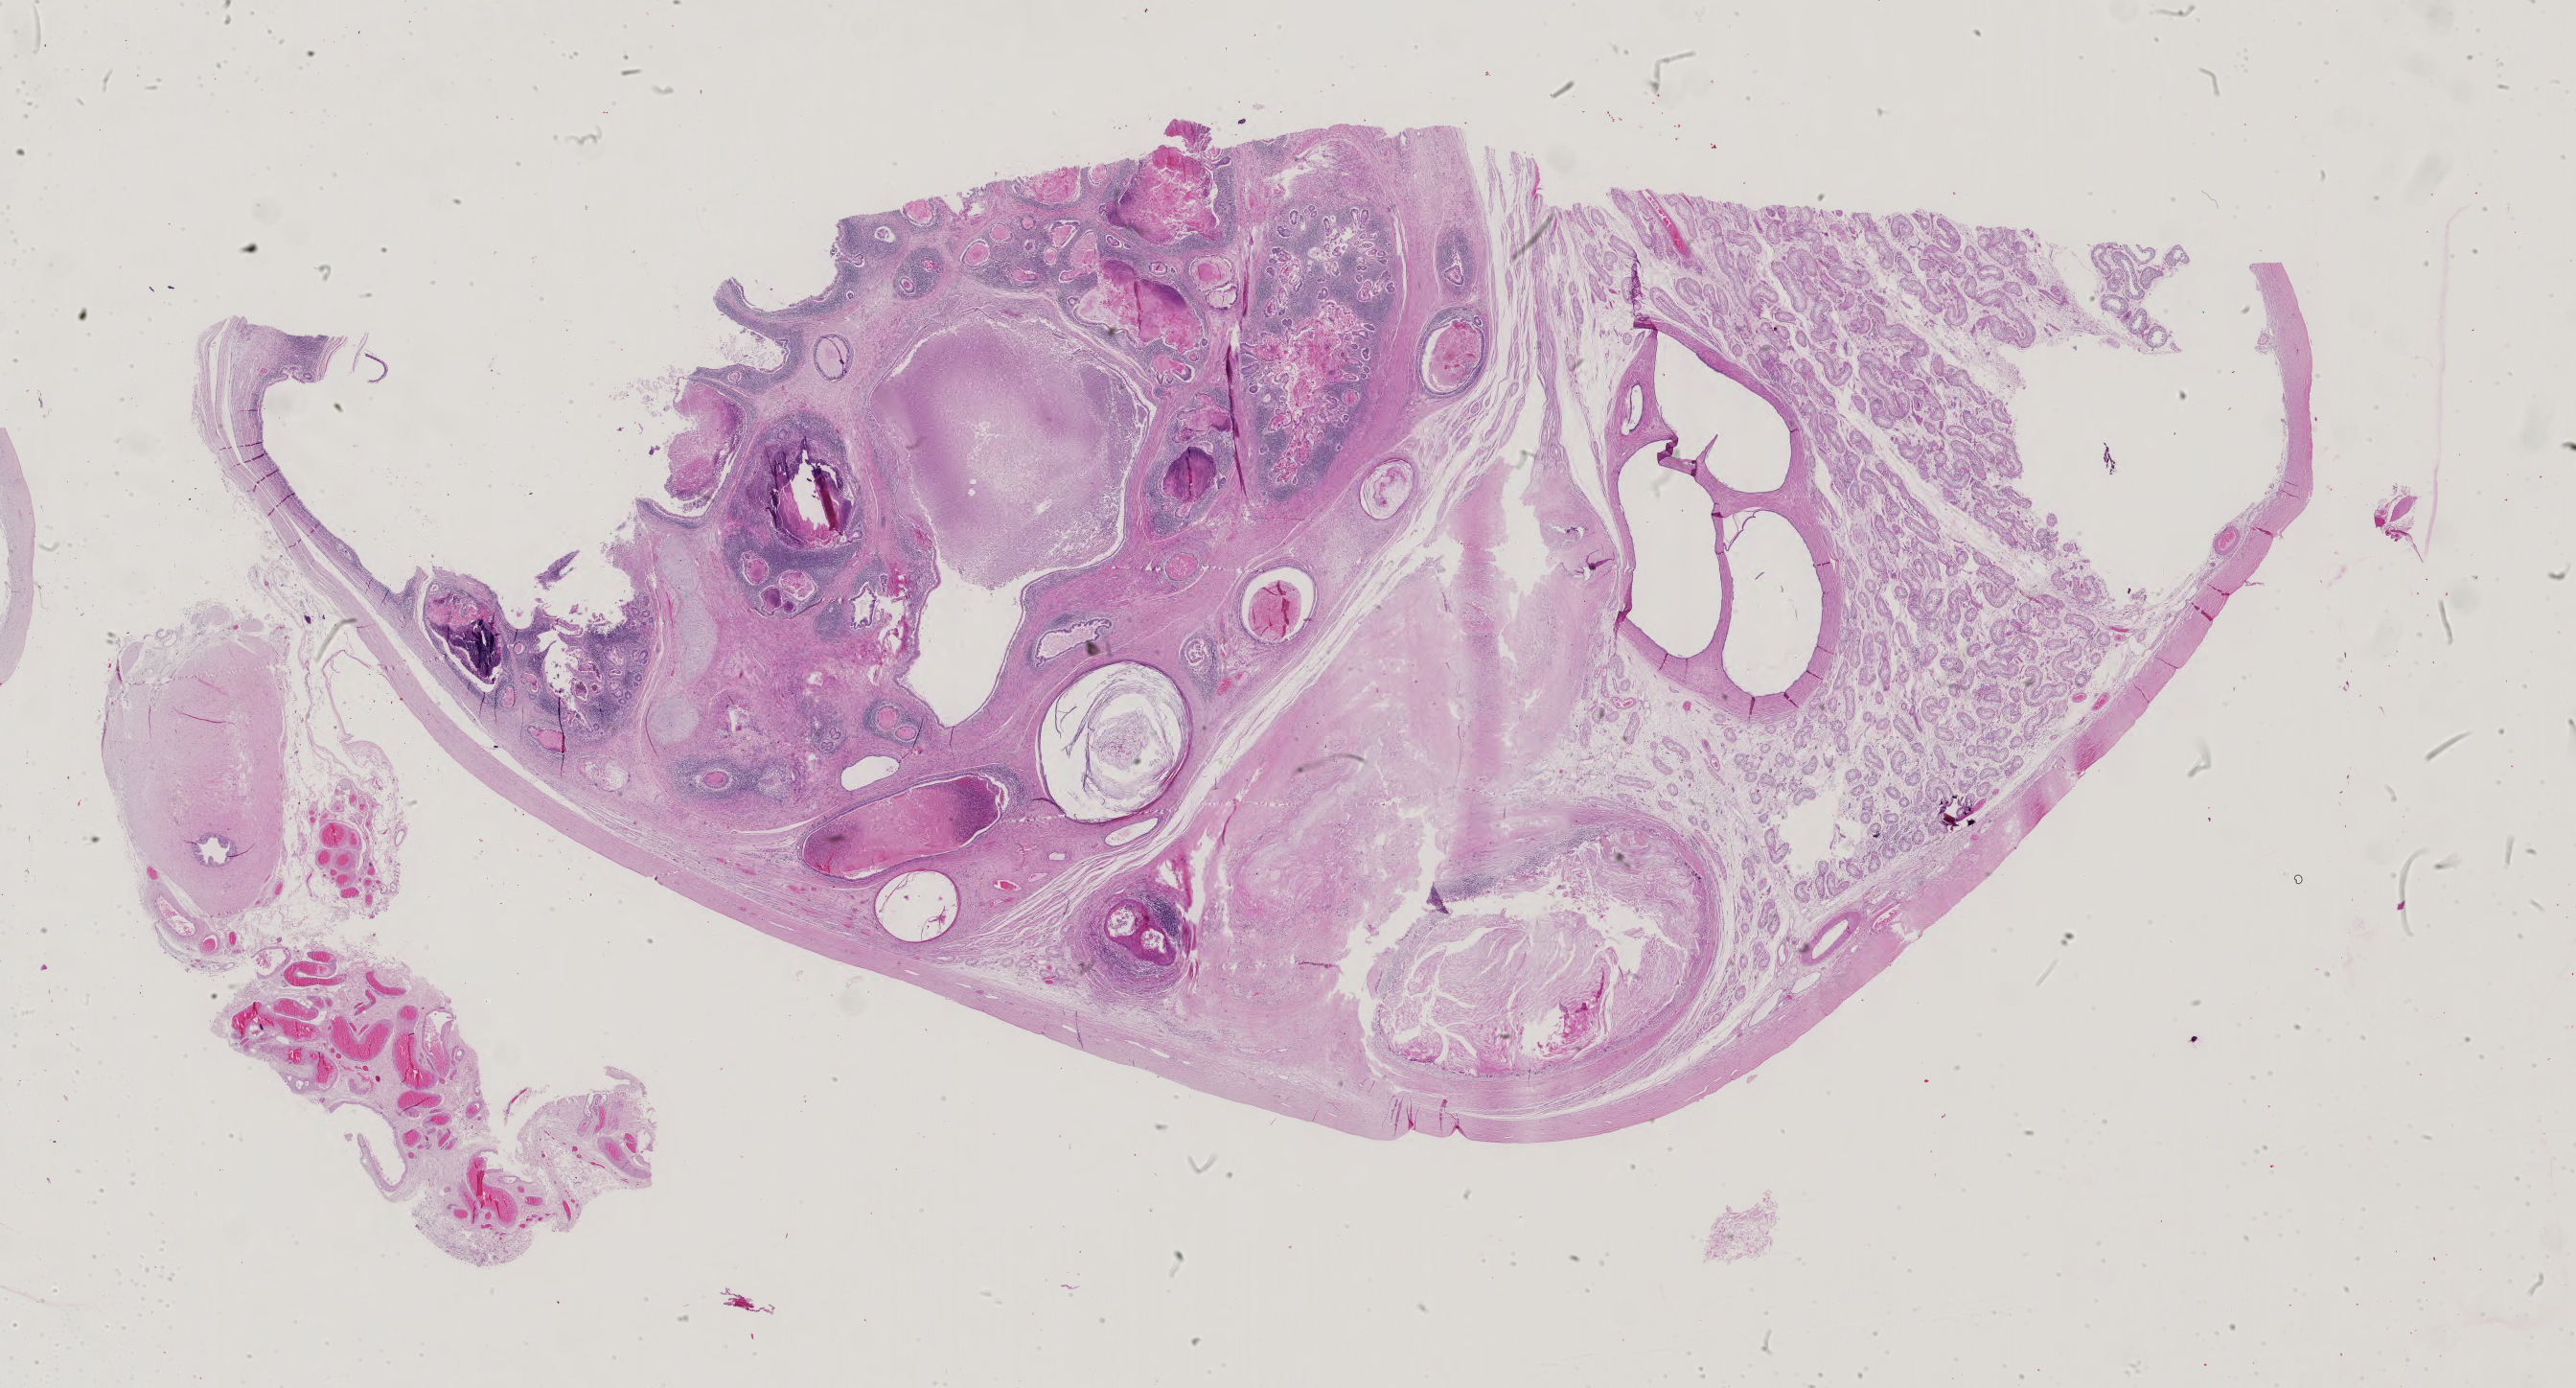
Whole-slide histology image, Hematoxylin and eosin (H&E) stained — low-resolution overview of the scanned area, about 39.2 x 21.1 mm. Male patient.
Specimen: FFPE section; primary tumour sample from the testis.